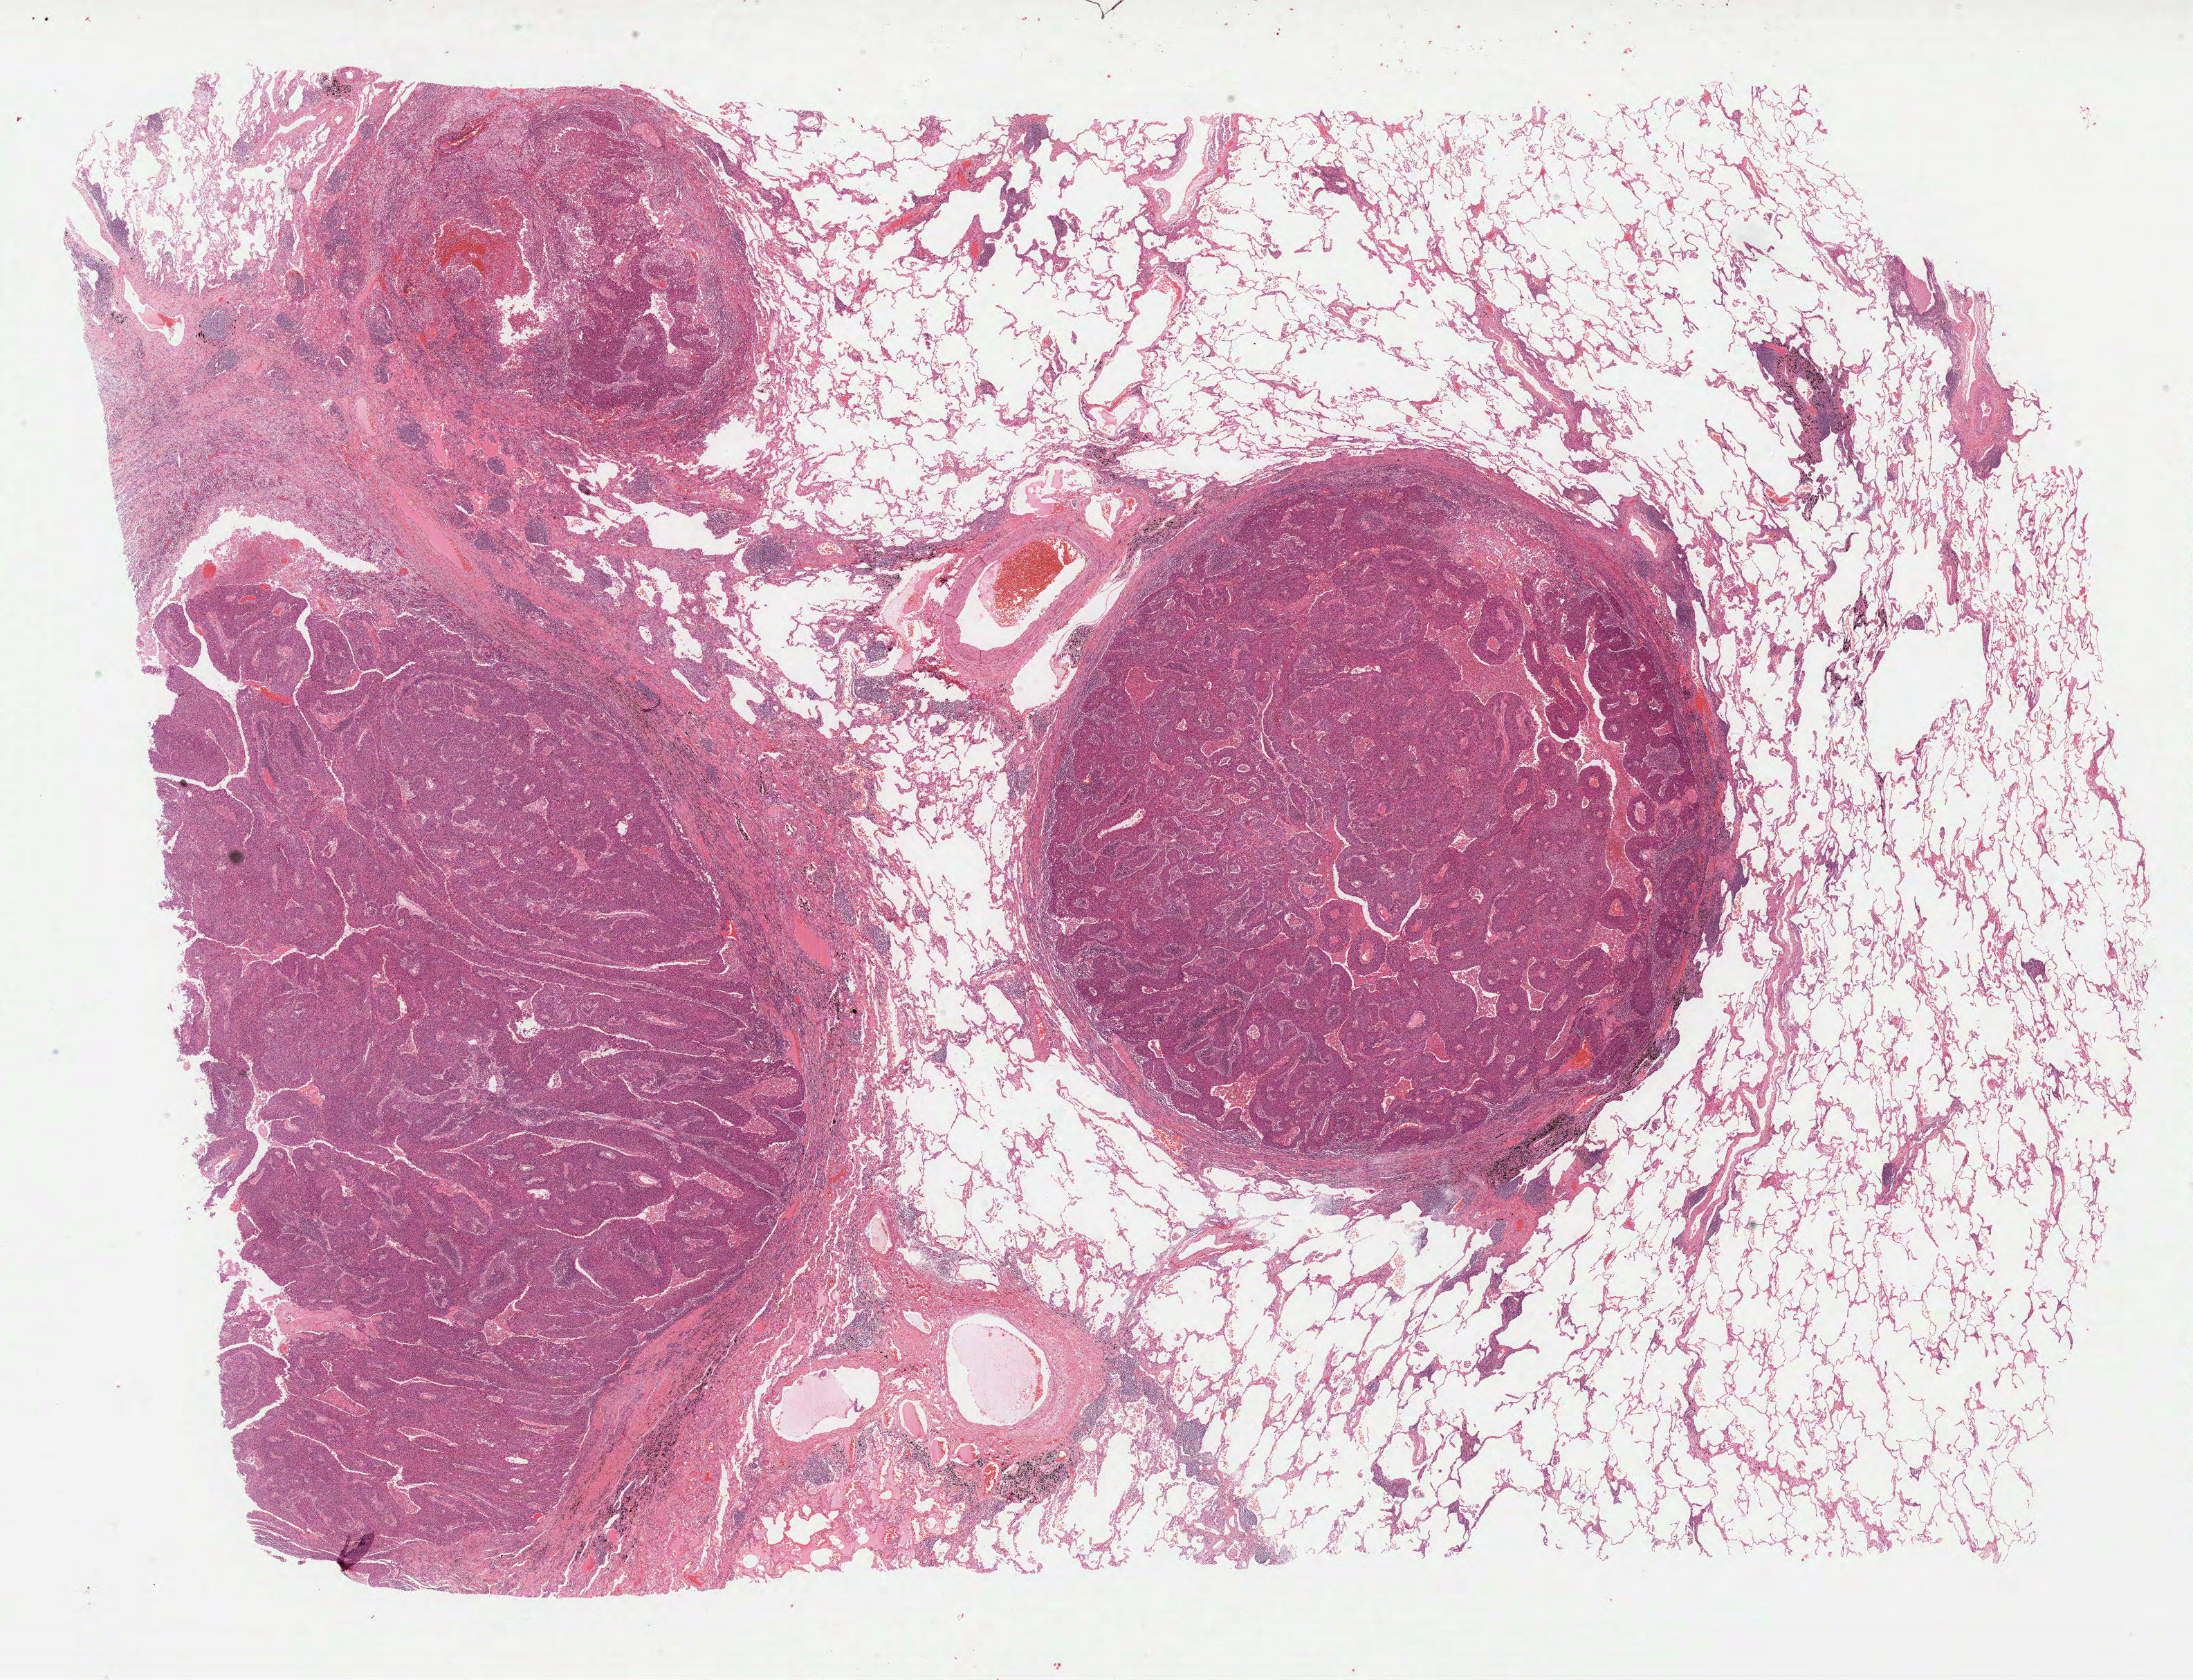
Digitized H&E-stained tissue section (whole slide) — shown as a low-resolution overview of the whole scanned area (about 25.6 x 19.6 mm); formalin-fixed paraffin-embedded (FFPE) diagnostic section; sample: primary tumour, lung. Male, age 83 years at initial diagnosis.
• AJCC pathologic stage: IIB
• diagnosis: Squamous cell carcinoma, NOS (upper lobe, lung)
• laterality: left